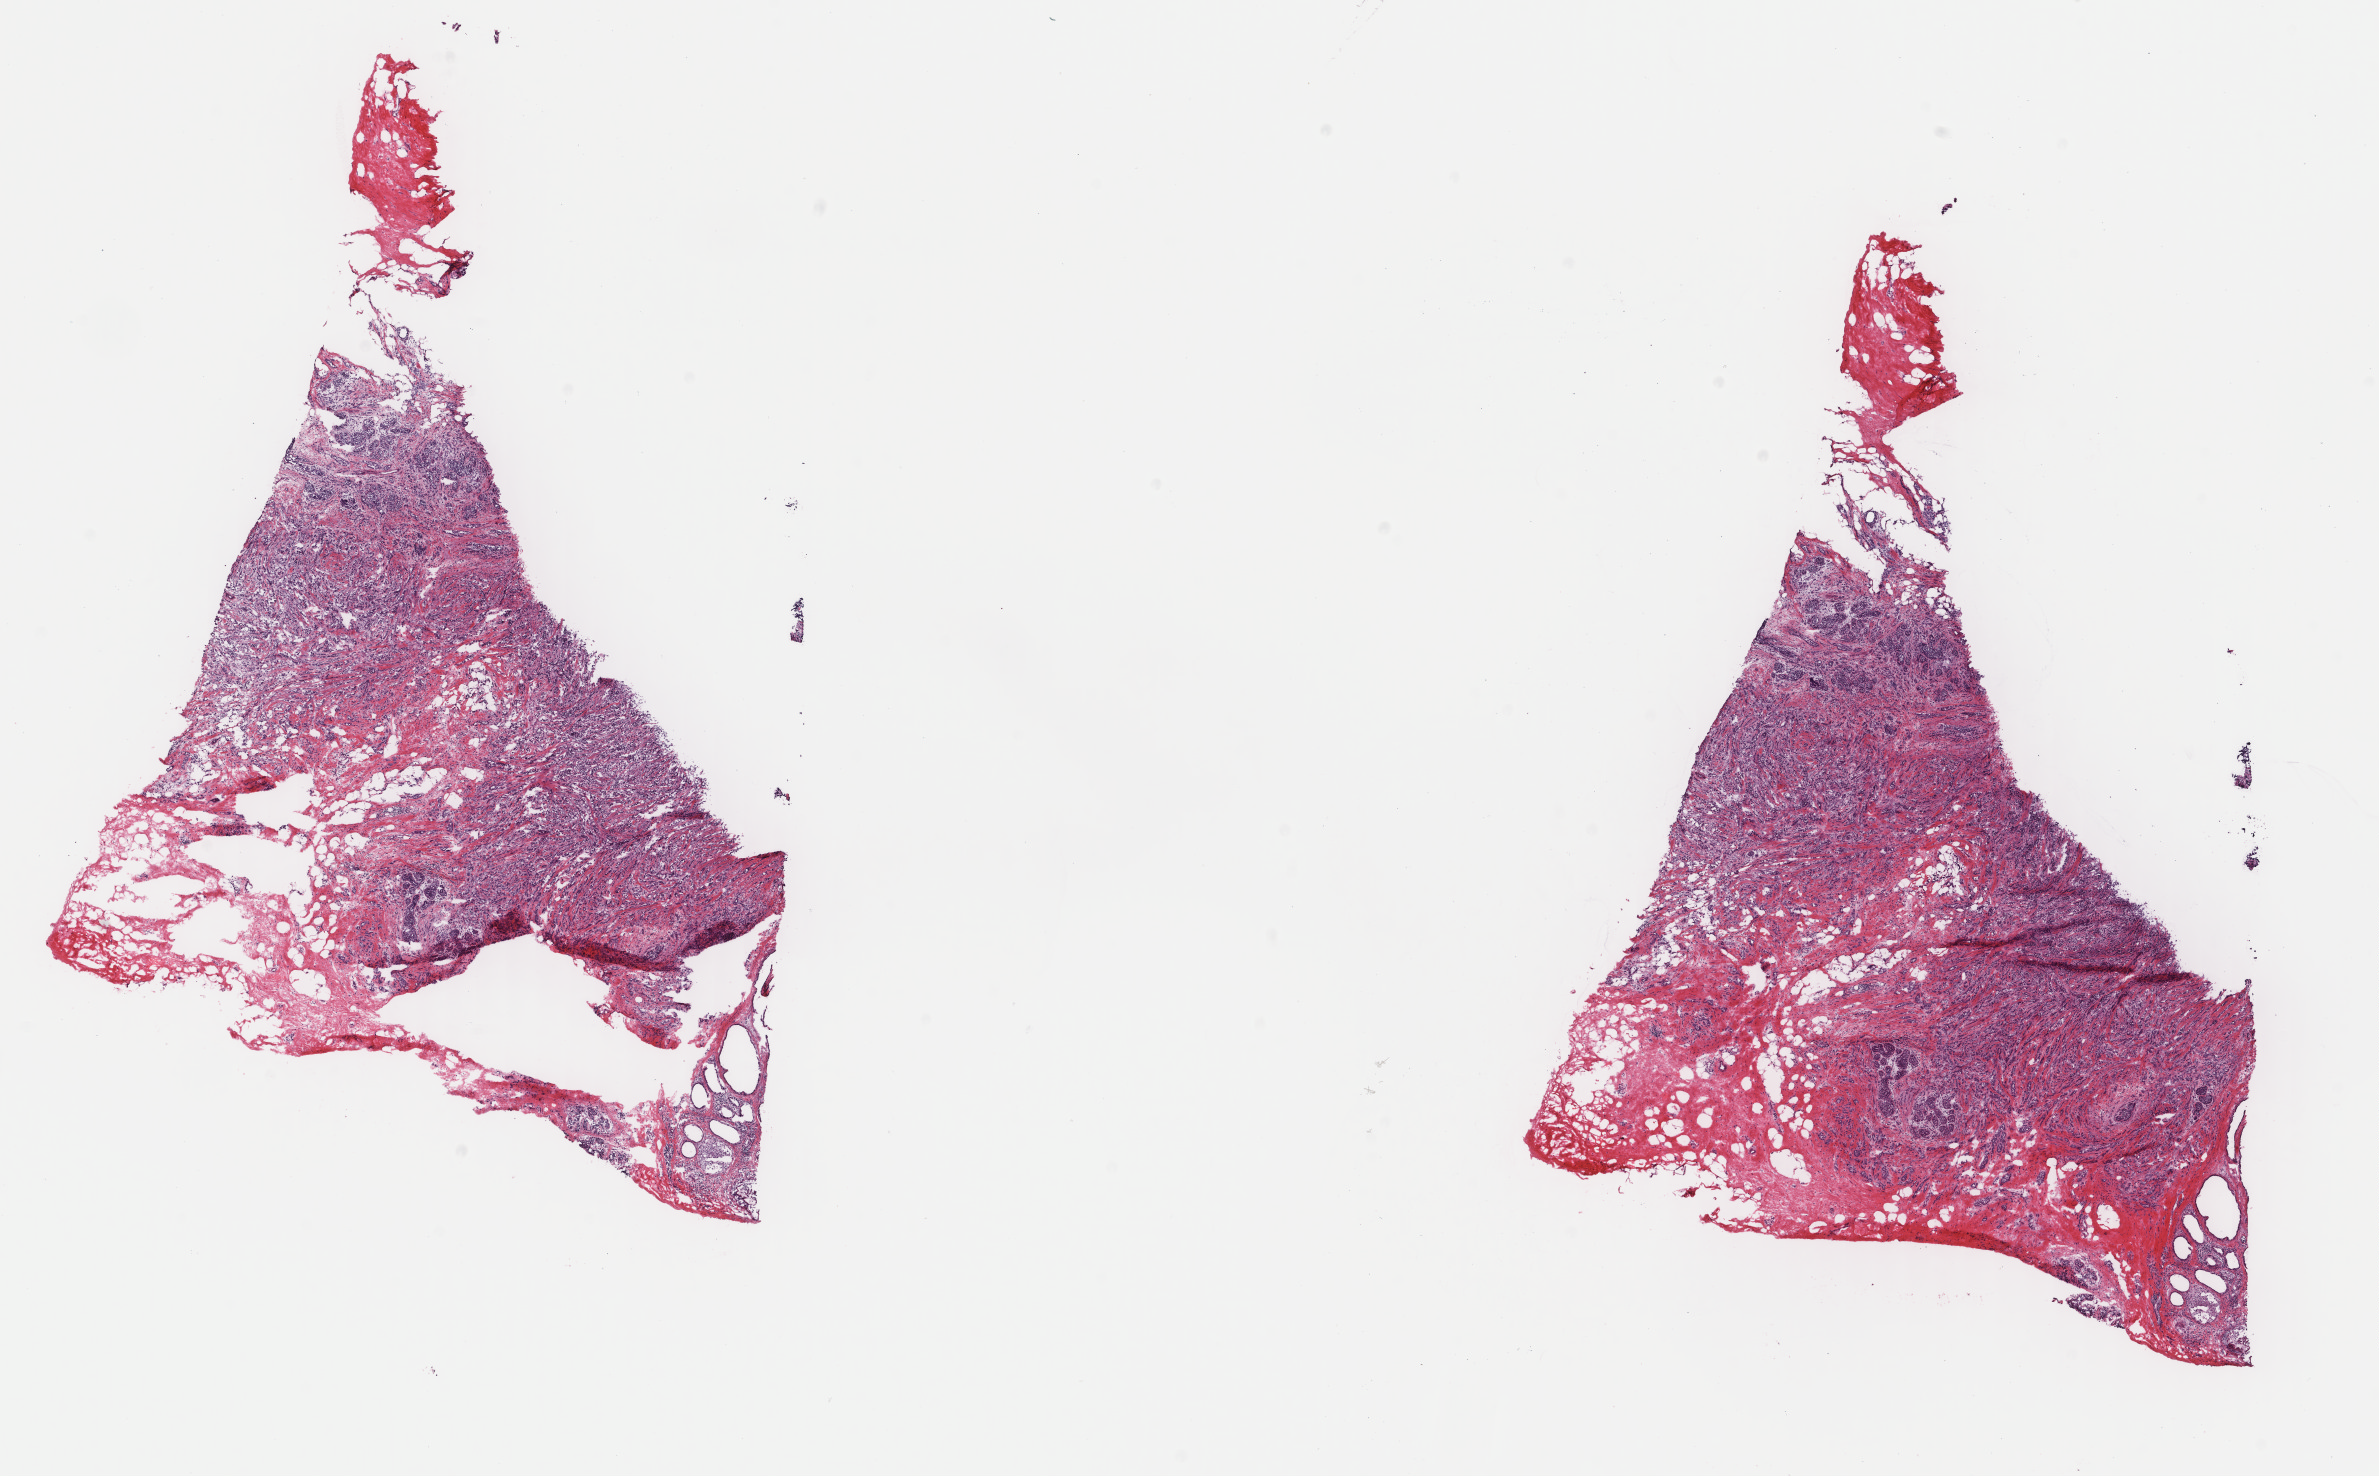
H&E whole-slide image — whole scanned area (about 18.9 x 11.7 mm) shown as a low-resolution overview, frozen section from the top of the tissue portion, sample: primary tumour, breast. Female patient; age at initial diagnosis 49 years. Composition of this section per pathologist review: tumour cells 60%, tumour nuclei 75%, normal cells 8%, stromal cells 32%, necrosis 0%. Inflammatory infiltration, as recorded: lymphocyte infiltration 1%, monocyte infiltration 2%, neutrophil infiltration 0%.
Lymph nodes positive (case pathology): 1 of 3 examined. TNM: T1 N1 M0. AJCC pathologic stage: II (6th edition). Histologic diagnosis: Lobular carcinoma, NOS.